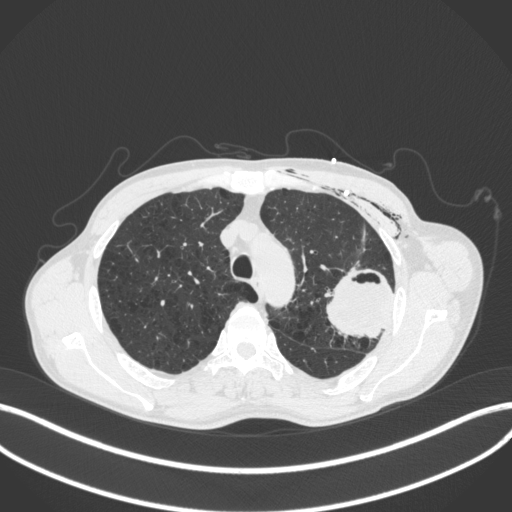
Chest CT, one axial slice; slice 305 of 416 in the series (ordered by position); reconstruction kernel B31f; lung window (W 1500 / L -600 HU); 512 × 512 image matrix, field of view 400 × 400 mm. Male patient, age 58 years. Case-level facts recorded for this patient, not image findings: clinical TNM (as recorded): T3 N0 M0.
Structures marked on this image (rectangle marked by the reading radiologist):
- lung tumour (recorded histology: adenocarcinoma): bounding box [x1, y1, x2, y2] px = [323, 267, 396, 339]